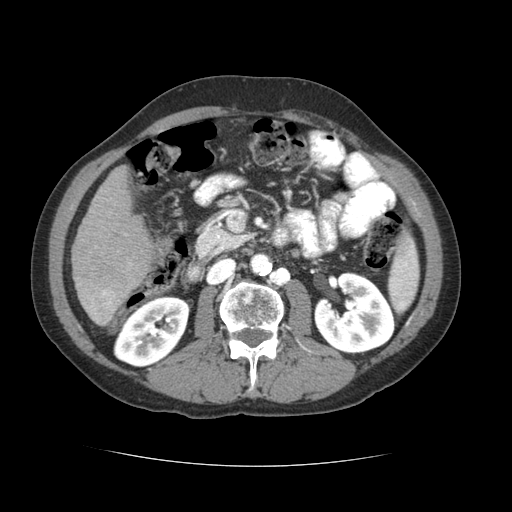
Contrast-enhanced abdominal CT (liver protocol), one axial slice; slice 21 of 69 in the series (ordered by position); reconstruction kernel STANDARD; soft-tissue window (W 400 / L 40 HU); 2.5 mm slice thickness; 512 × 512 image matrix, field of view 360 × 360 mm. Case-level facts recorded for this patient, not image findings: diagnosis: hepatocellular carcinoma (patient treated with transarterial chemoembolisation; whether this scan precedes or follows treatment is not stated here); TNM stage (as recorded): Stage-II; Child-Pugh class: B; tumour differentiation: poorly differentiated; tumour nodularity: multinodular.
Outlined on this slice (semi-automatic segmentation, software-assisted and operator-edited):
- liver parenchyma outside the tumour (the mass and vessels are separate outlines, so this box may not span the whole liver): bounding box (x1, y1, x2, y2) in pixels: (72, 166, 152, 326)
- liver vessels: (89, 289, 115, 321)